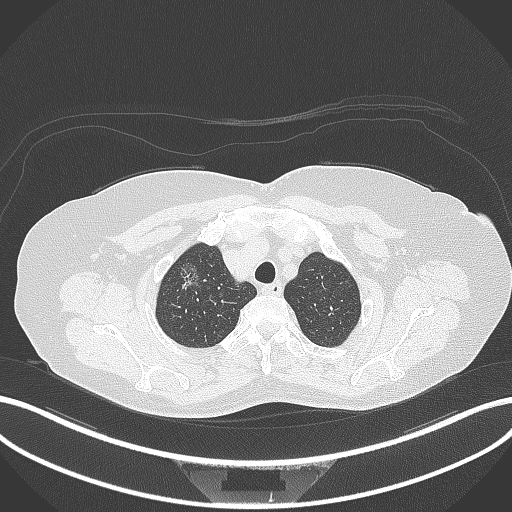
Chest CT, one axial slice; position 302 of 365 along the scan axis; reconstruction kernel B70f; lung window (W 1500 / L -600 HU); 1 mm slice thickness; 512 × 512 image matrix. Female patient, age 62 years. From the clinical record (not read from this slice): clinical TNM (as recorded): T1c N0 M0.
Outlined on this slice (bounding box drawn by a radiologist):
- lung tumour (recorded histology: adenocarcinoma): box from (x=176, y=253) to (x=210, y=296) px